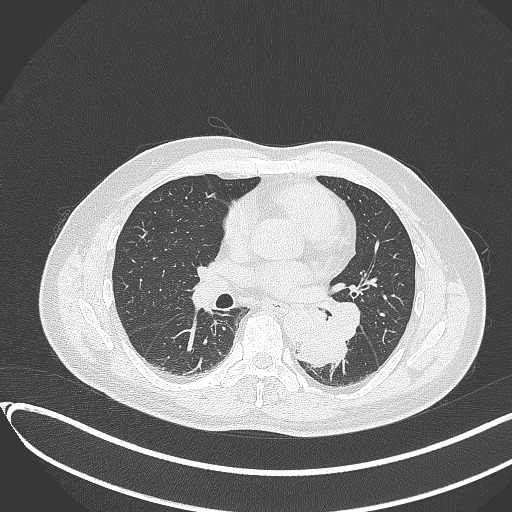
Chest CT, one axial slice. Slice 176 of 417 in the series (ordered by position). Reconstruction kernel B70f. 120 kVp. Lung window (W 1500 / L -600 HU). 1 mm slice thickness. 512 × 512 image matrix. Male patient, age 54 years. Case-level facts recorded for this patient, not image findings: clinical TNM (as recorded): T3 N0 M0.
Structures marked on this image (bounding box drawn by a radiologist):
- lung tumour (recorded histology: squamous cell carcinoma): box from (x=288, y=307) to (x=351, y=368) px